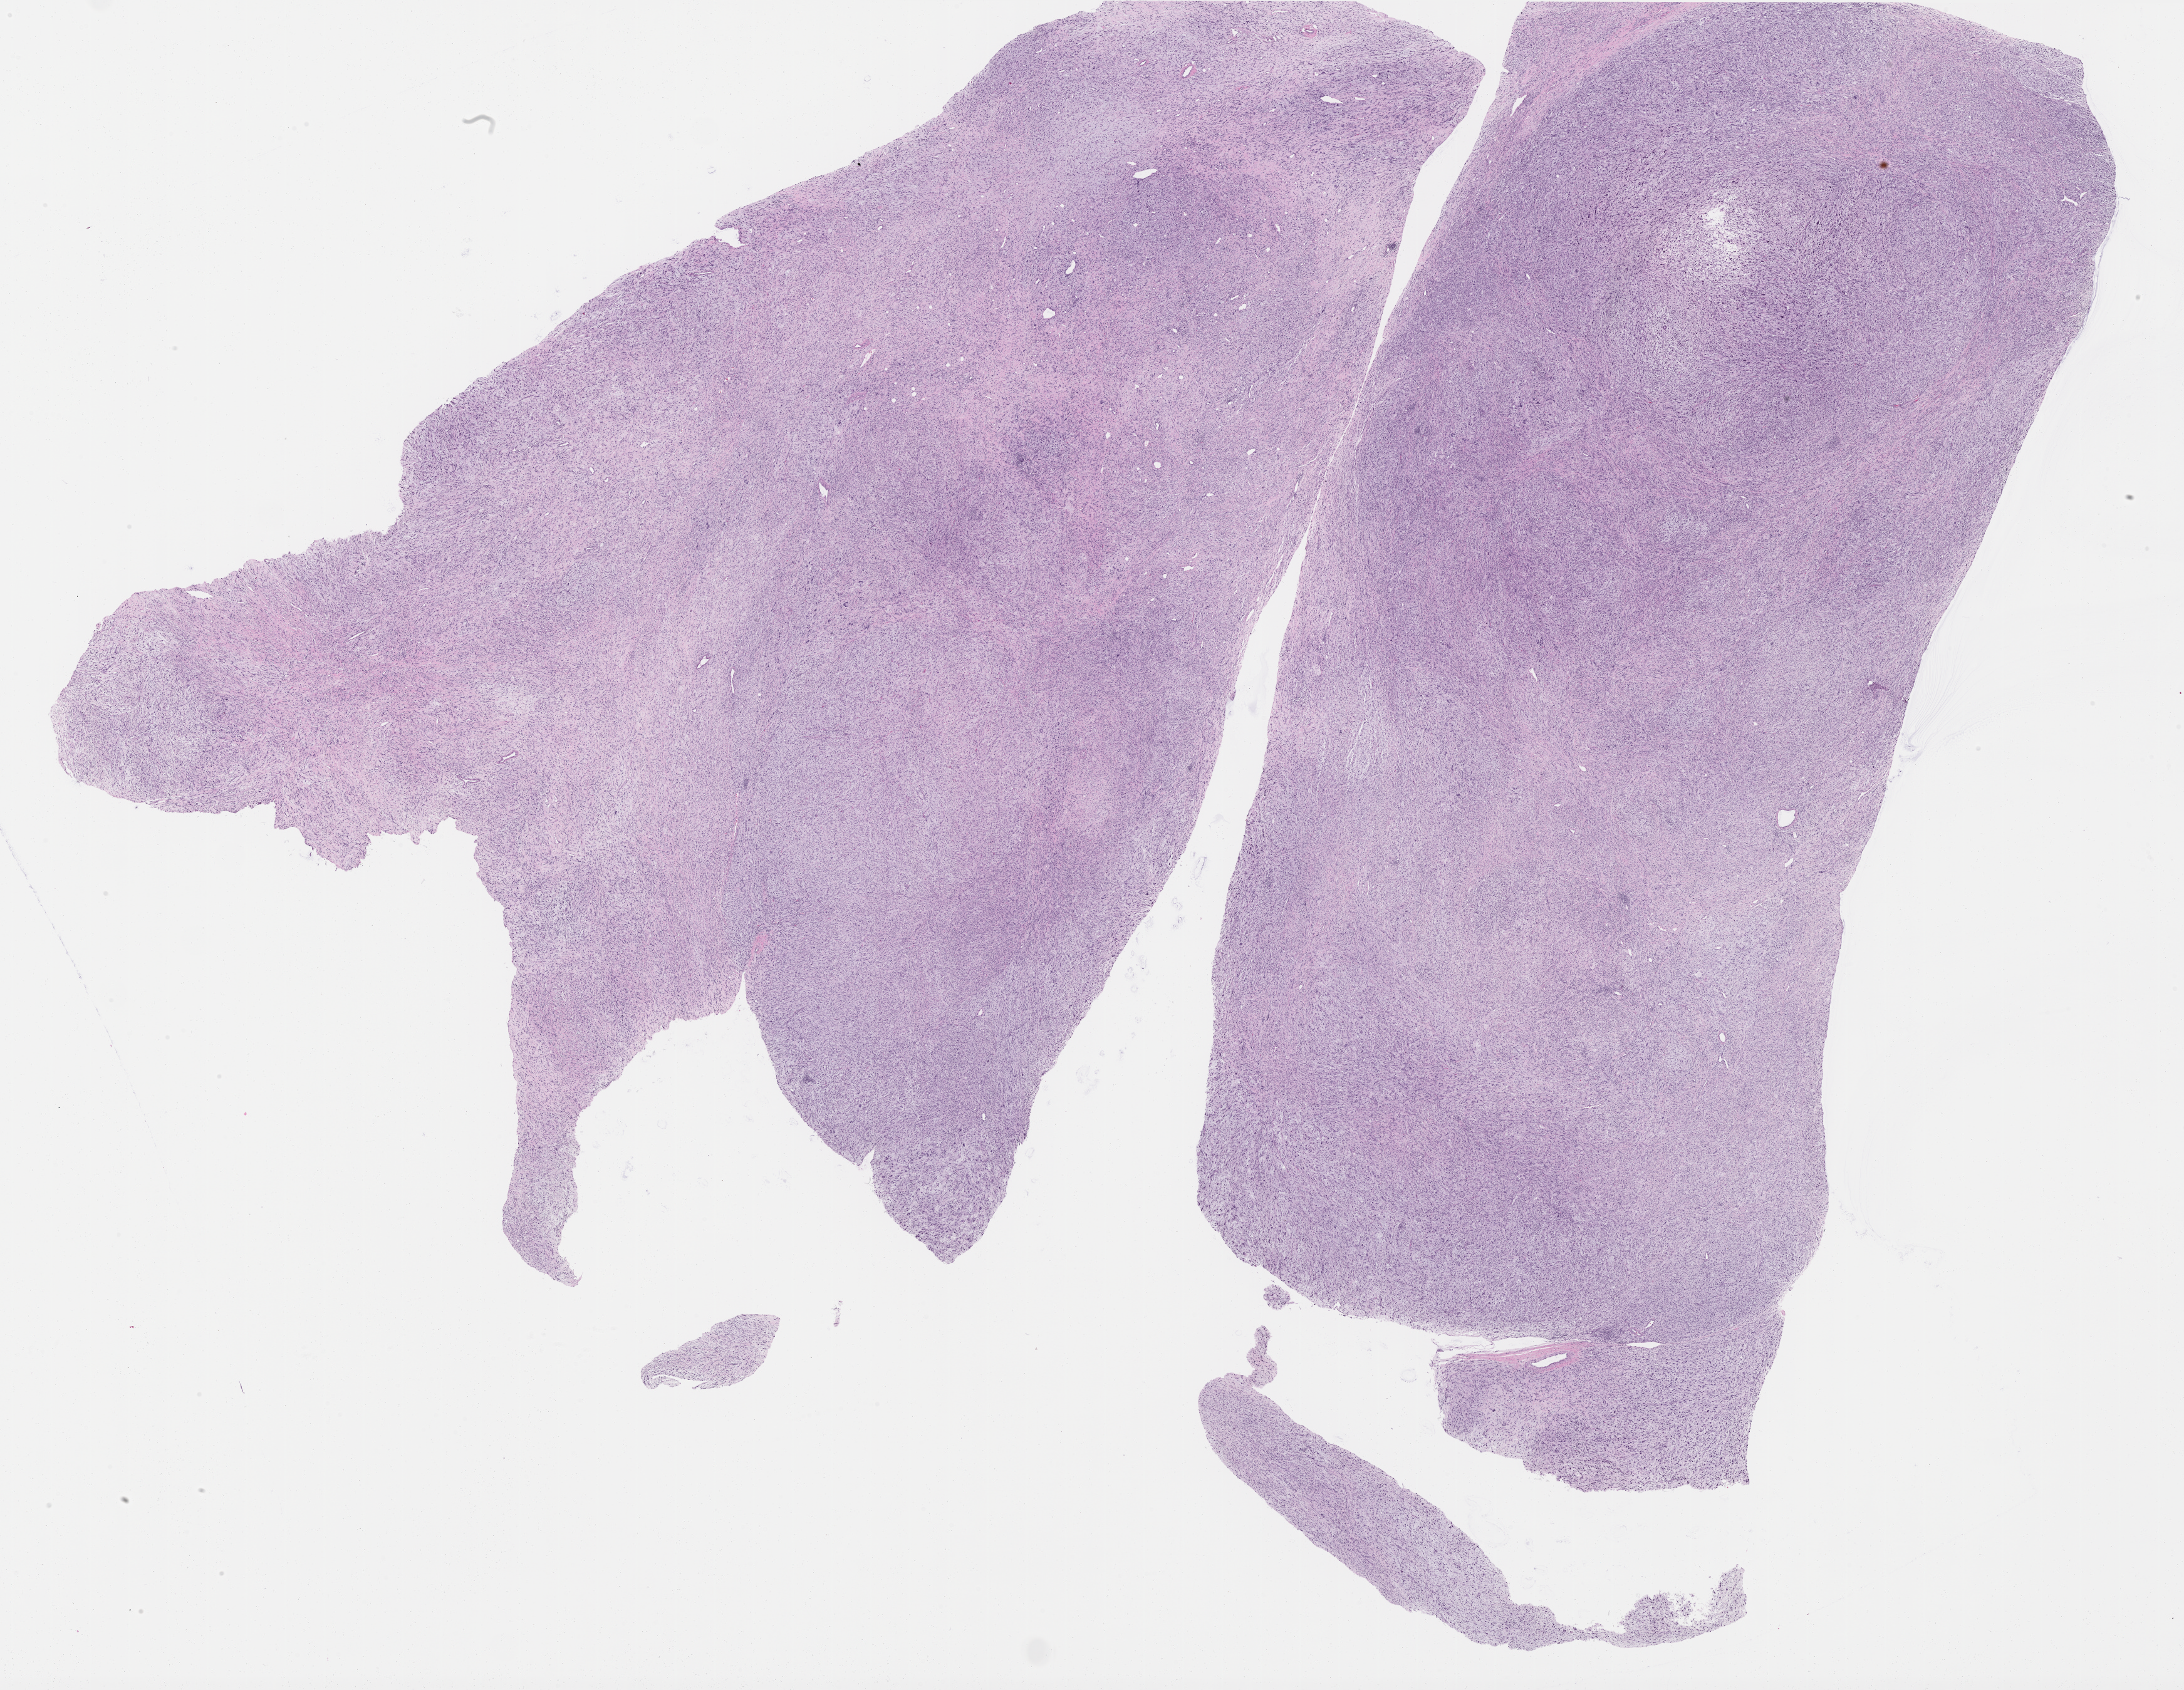
Digitized Hematoxylin and eosin (H&E) stained tissue section (whole slide), shown as a low-resolution overview of the whole scanned area (about 28.0 x 21.7 mm, slide scanned at 40x); formalin-fixed paraffin-embedded (FFPE) diagnostic section; primary tumour sample from the retroperitoneum and peritoneum. Female, age 79 years at initial diagnosis.
• pathologic diagnosis: Fibromyxosarcoma (retroperitoneum)